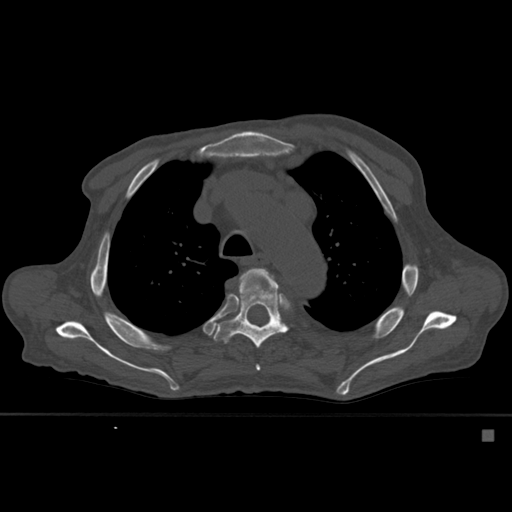
CT including the spine, one axial slice; slice 404 of 527 in the series (ordered by position); bone window (W 1800 / L 400 HU); 1.5 mm slice thickness; 512 × 512 image matrix, field of view 373 × 373 mm. Patient: male, 78 years. Case-level facts recorded for this patient, not image findings: primary cancer: prostate.
Outlined on this slice (semi-automatic segmentation, software-assisted and operator-edited):
- T4 vertebra: box from (x=240, y=268) to (x=277, y=371) px
- T5 vertebra: (x=213, y=268)–(x=288, y=349)